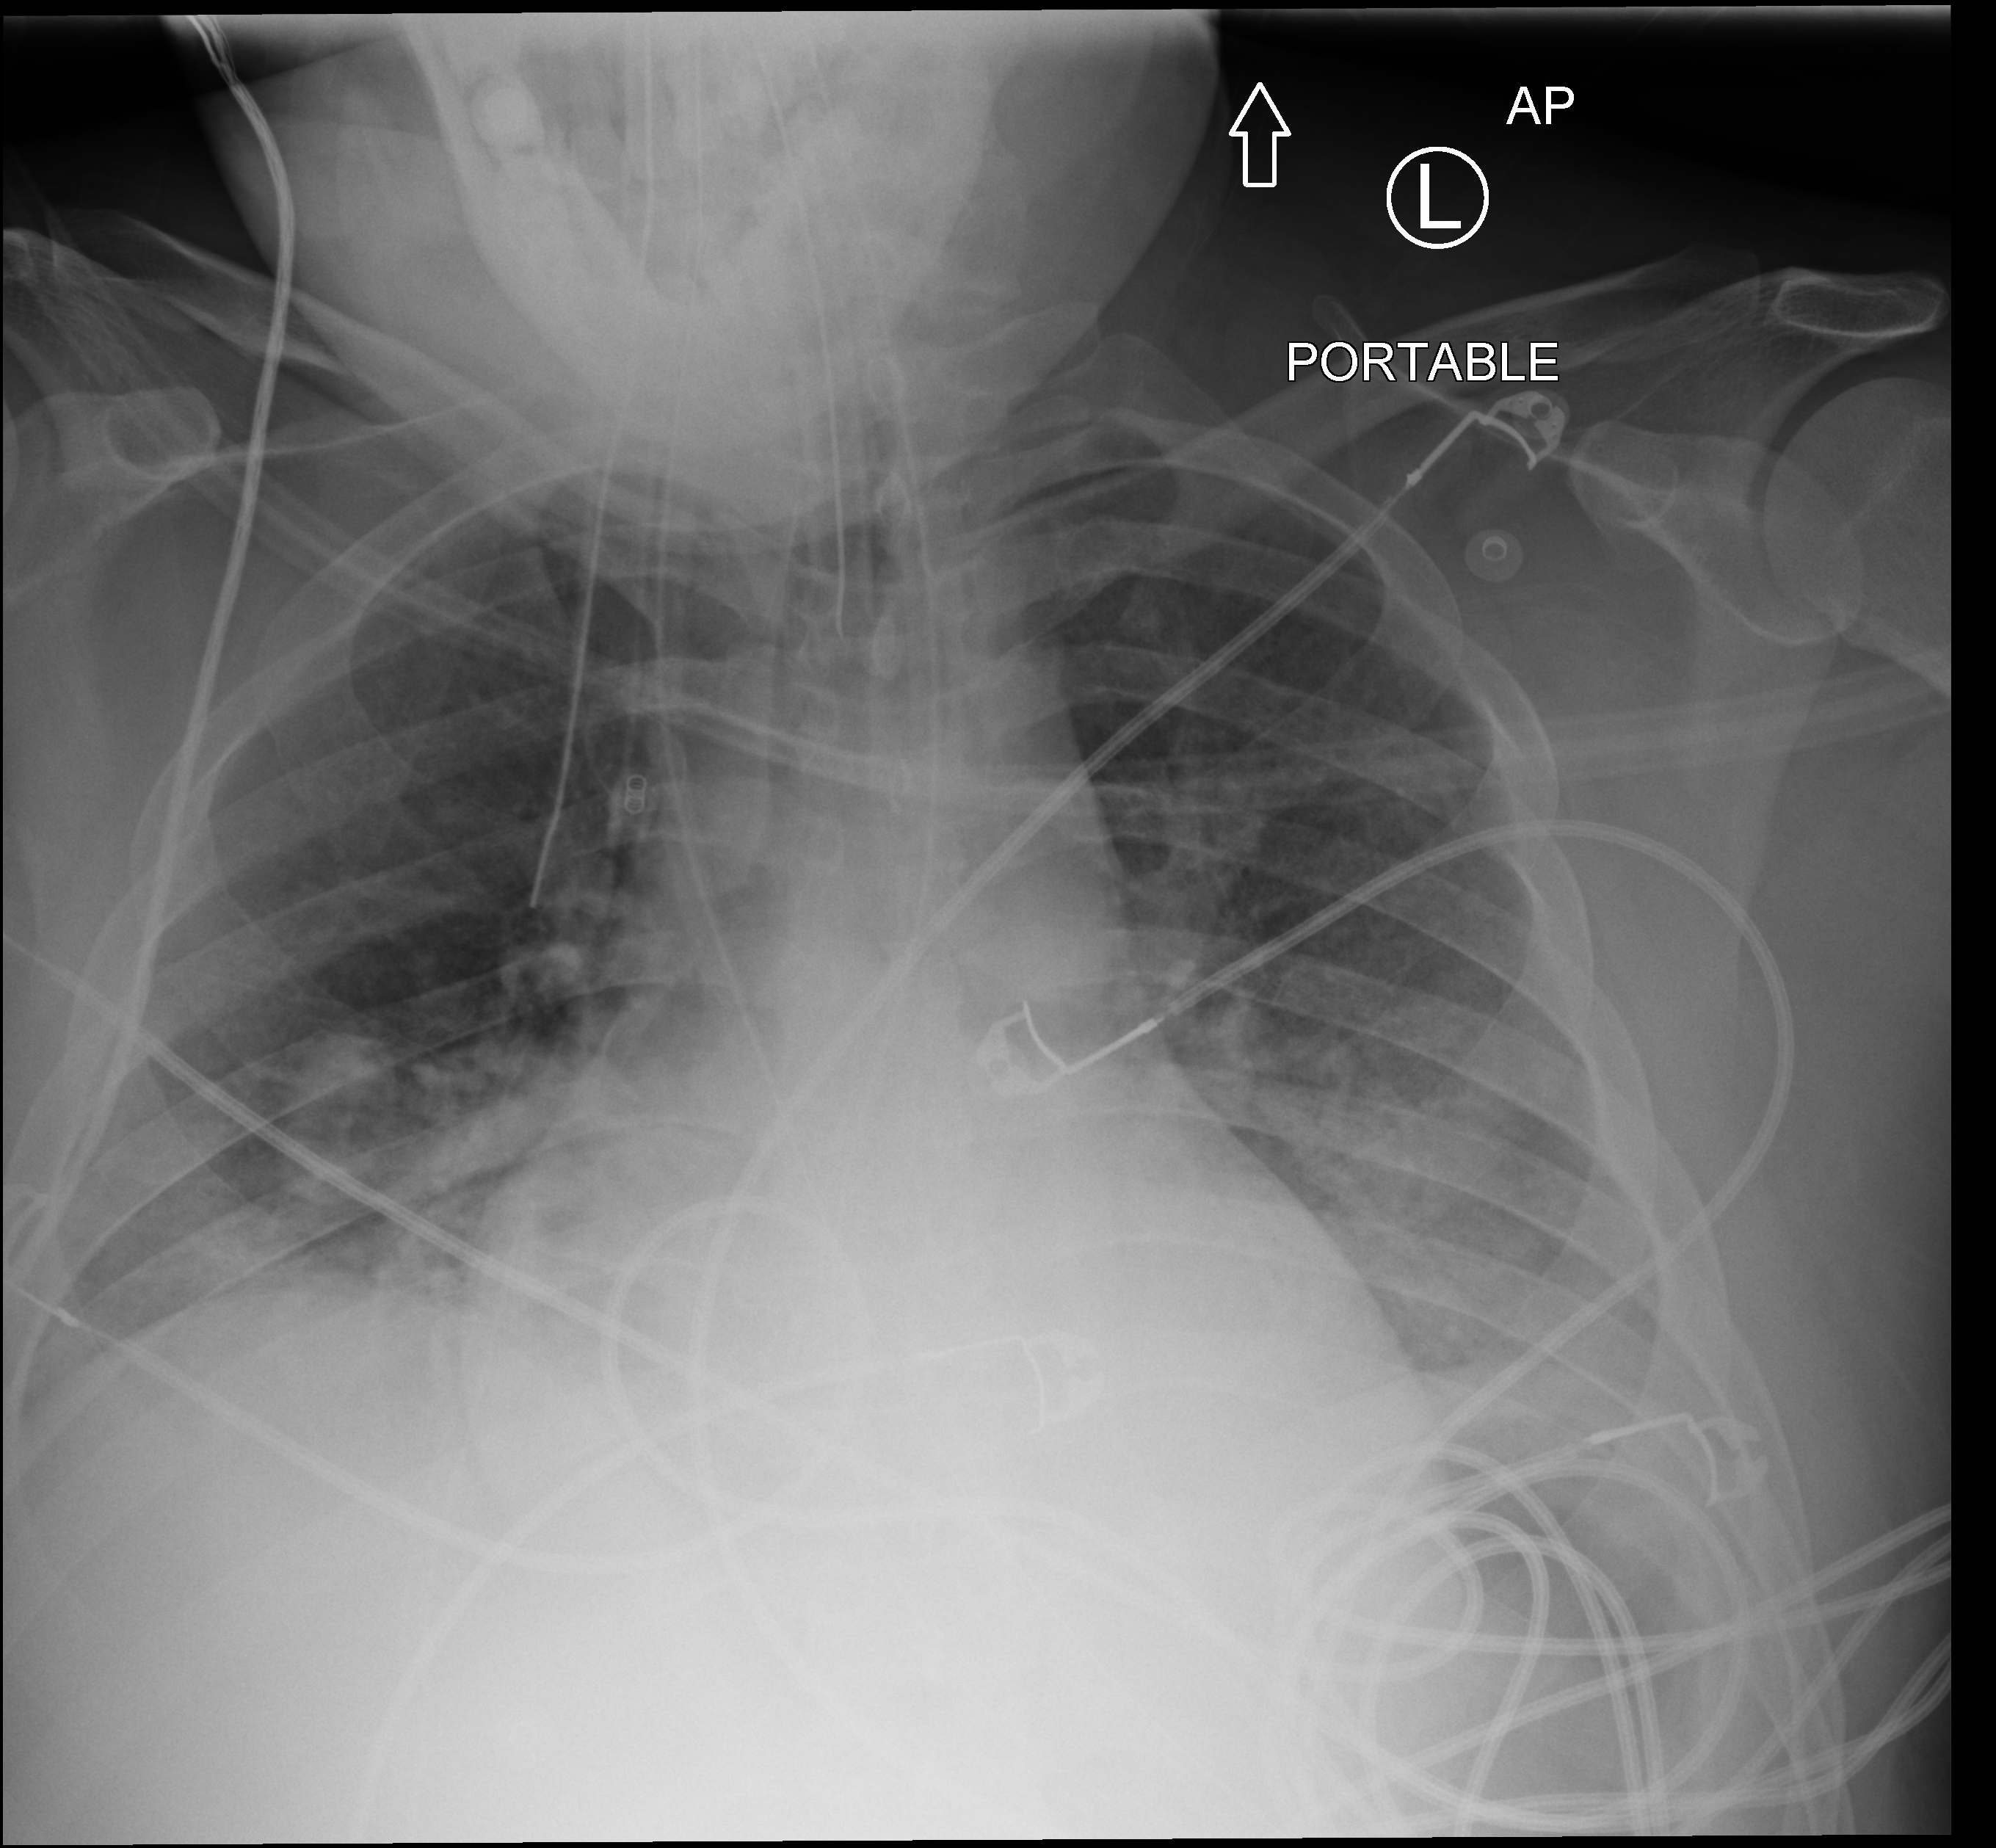
Chest X-ray (portable). Male patient hospitalised with COVID-19, age 18–59 years.
Hospital-stay facts (about this admission, not read from this image; timing relative to this image not recorded):
- diabetes (admission record): no
- admitted to intensive care during this hospital stay: yes
- mechanically ventilated during this hospital stay: yes